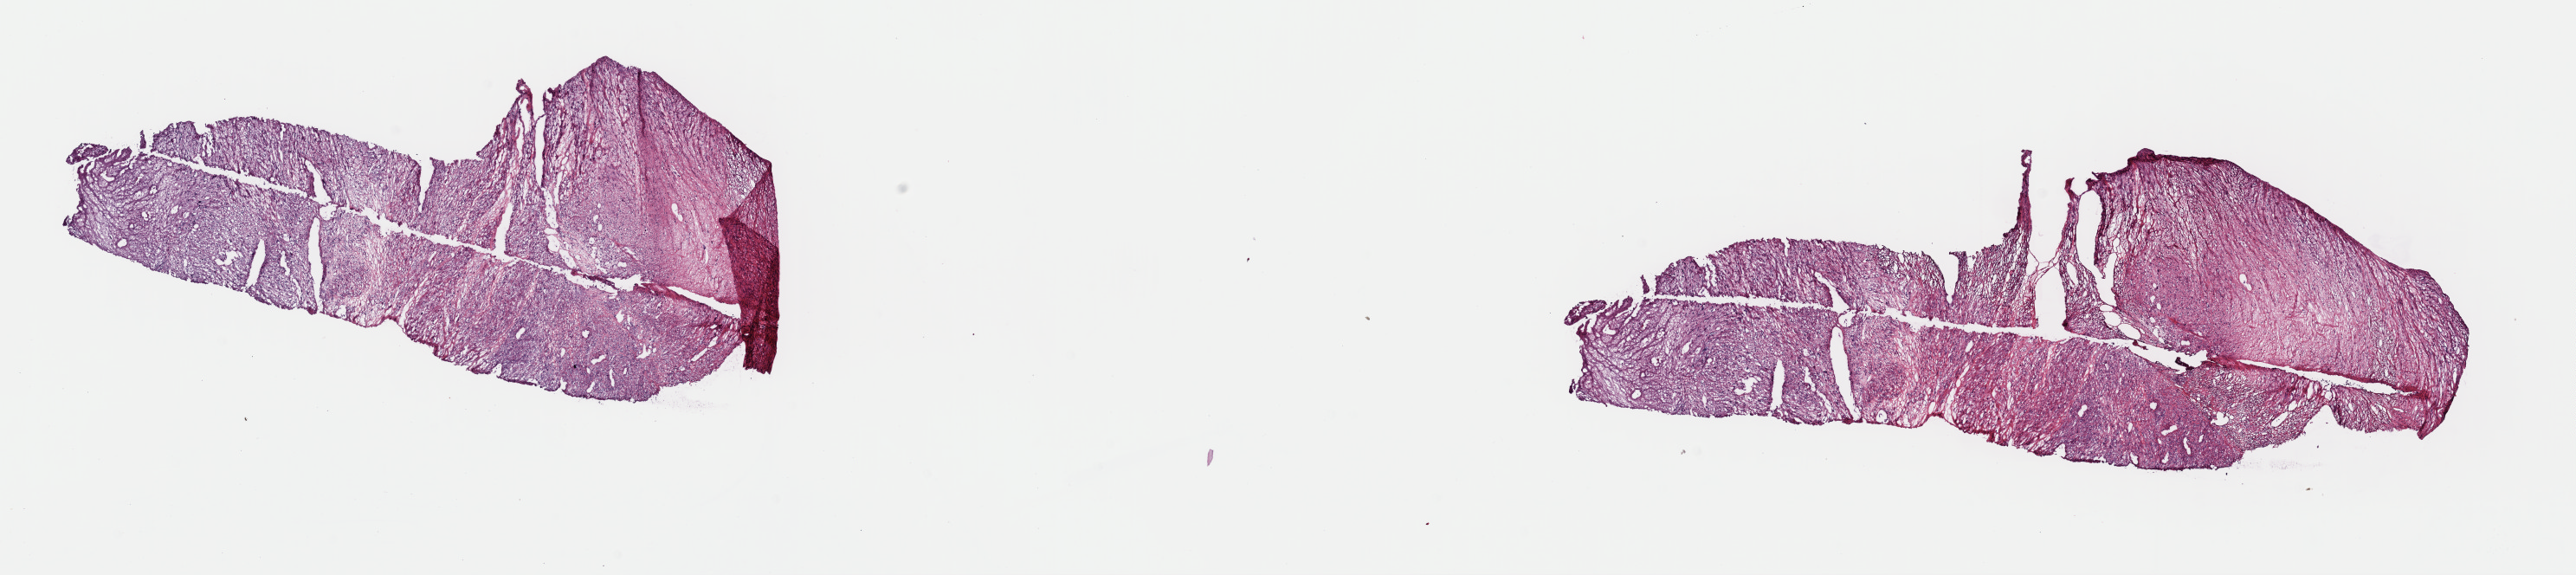
Hematoxylin and eosin (H&E) stained whole-slide image — a low-resolution overview of the entire scanned area, about 23.5 x 5.2 mm (slide scanned at 40x). Frozen section from the top of the tissue portion. Connective, subcutaneous and other soft tissues, primary tumour sample. Female, age 49 years at initial diagnosis. Slide review estimates, as recorded: tumour cells 100%, tumour nuclei 94%, normal cells 0%, stromal cells 0%, necrosis 0%. Infiltration values recorded for this section: lymphocyte infiltration 0%, monocyte infiltration 0%, neutrophil infiltration 0%.
Pathologic diagnosis: Leiomyosarcoma, NOS (connective, subcutaneous and other soft tissues of lower limb and hip).